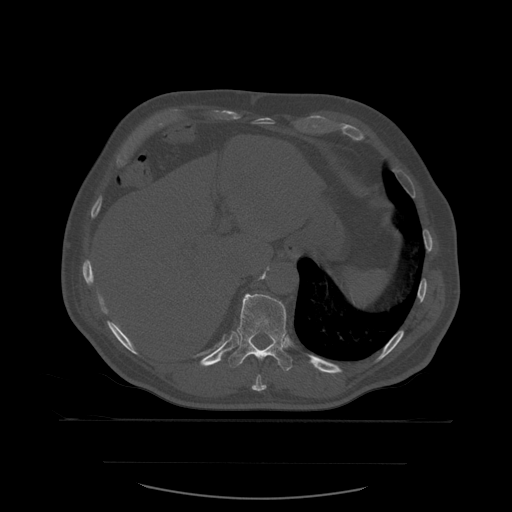
CT including the spine, one axial slice. Slice 300 of 590 in the series (ordered by position). Bone window (W 1800 / L 400 HU). 512 × 512 image matrix, field of view 479 × 479 mm. Patient age 71 years. Case-level facts recorded for this patient, not image findings: primary cancer: lung.
Structures marked on this image (semi-automatic segmentation, software-assisted and operator-edited):
- T10 vertebra: bounding box [x1, y1, x2, y2] px = [252, 375, 267, 392]
- T11 vertebra: [228, 294, 293, 371]